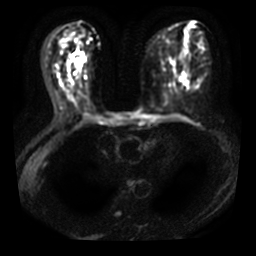
Breast MRI, one axial slice. Slice 16 of 40 in the series (ordered by position). Diffusion-weighted series; image 2 of 4 stored at this slice position (different b-values; order by instance number). 3 T. 5 mm slice thickness. 256 × 256 image matrix, field of view 320 × 320 mm. Female patient.
Structures marked on this image (manually delineated by an expert):
- tumour on diffusion-weighted imaging: box from (x=72, y=57) to (x=81, y=66) px